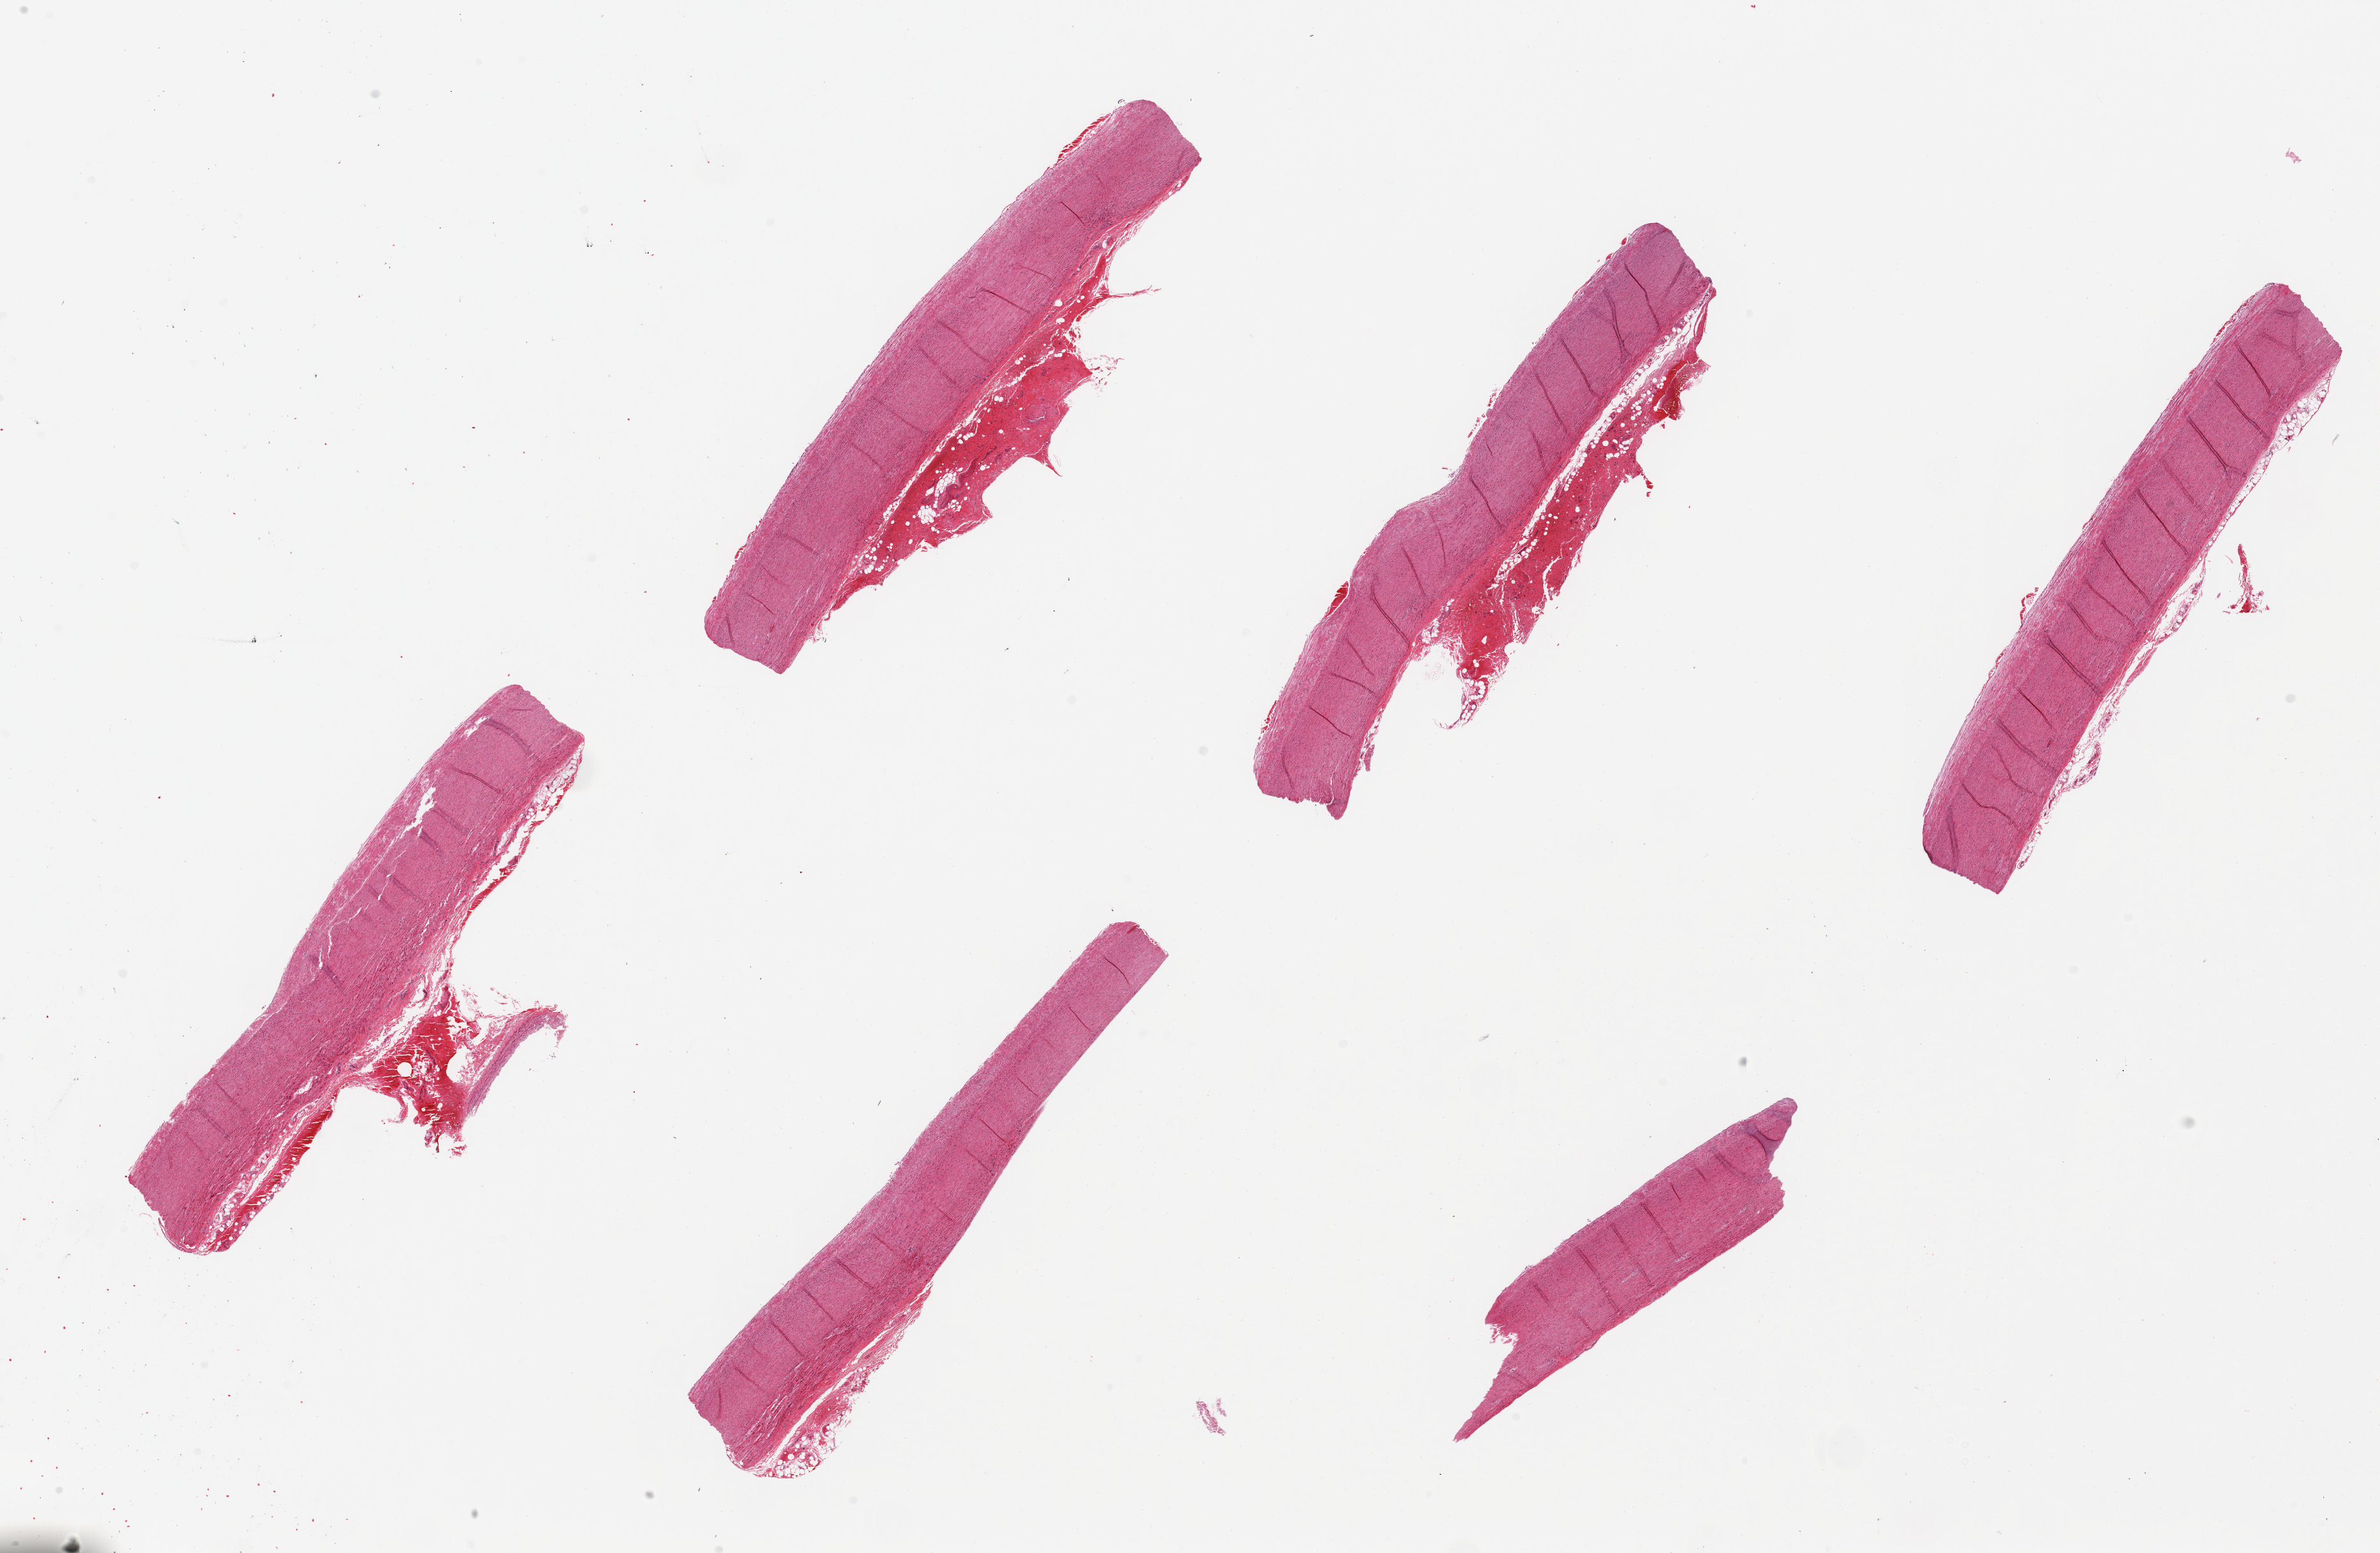
Haematoxylin and eosin whole-slide image — shown as a low-resolution overview of the whole scanned area (about 29.5 x 19.3 mm, acquisition: 20x scan), PAXgene-fixed paraffin-embedded (PFPE) section, target tissue: aorta, donor tissue sample.
Review note (as recorded): 6 pieces, up to 8x3mm.